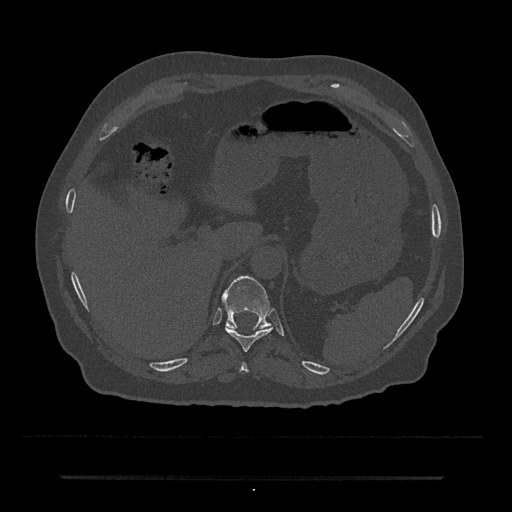
CT including the spine, one axial slice; position 211 of 797 along the scan axis; 120 kVp; bone window (W 1800 / L 400 HU); 512 × 512 image matrix, field of view 437 × 437 mm. Patient: male, 69 years. From the clinical record (not read from this slice): primary cancer: prostate.
Outlined on this slice (semi-automatically segmented with operator editing):
- T10 vertebra: box from (x=225, y=326) to (x=273, y=351) px
- T11 vertebra: (x=221, y=275)–(x=271, y=330)
- T9 vertebra: (x=240, y=362)–(x=248, y=373)